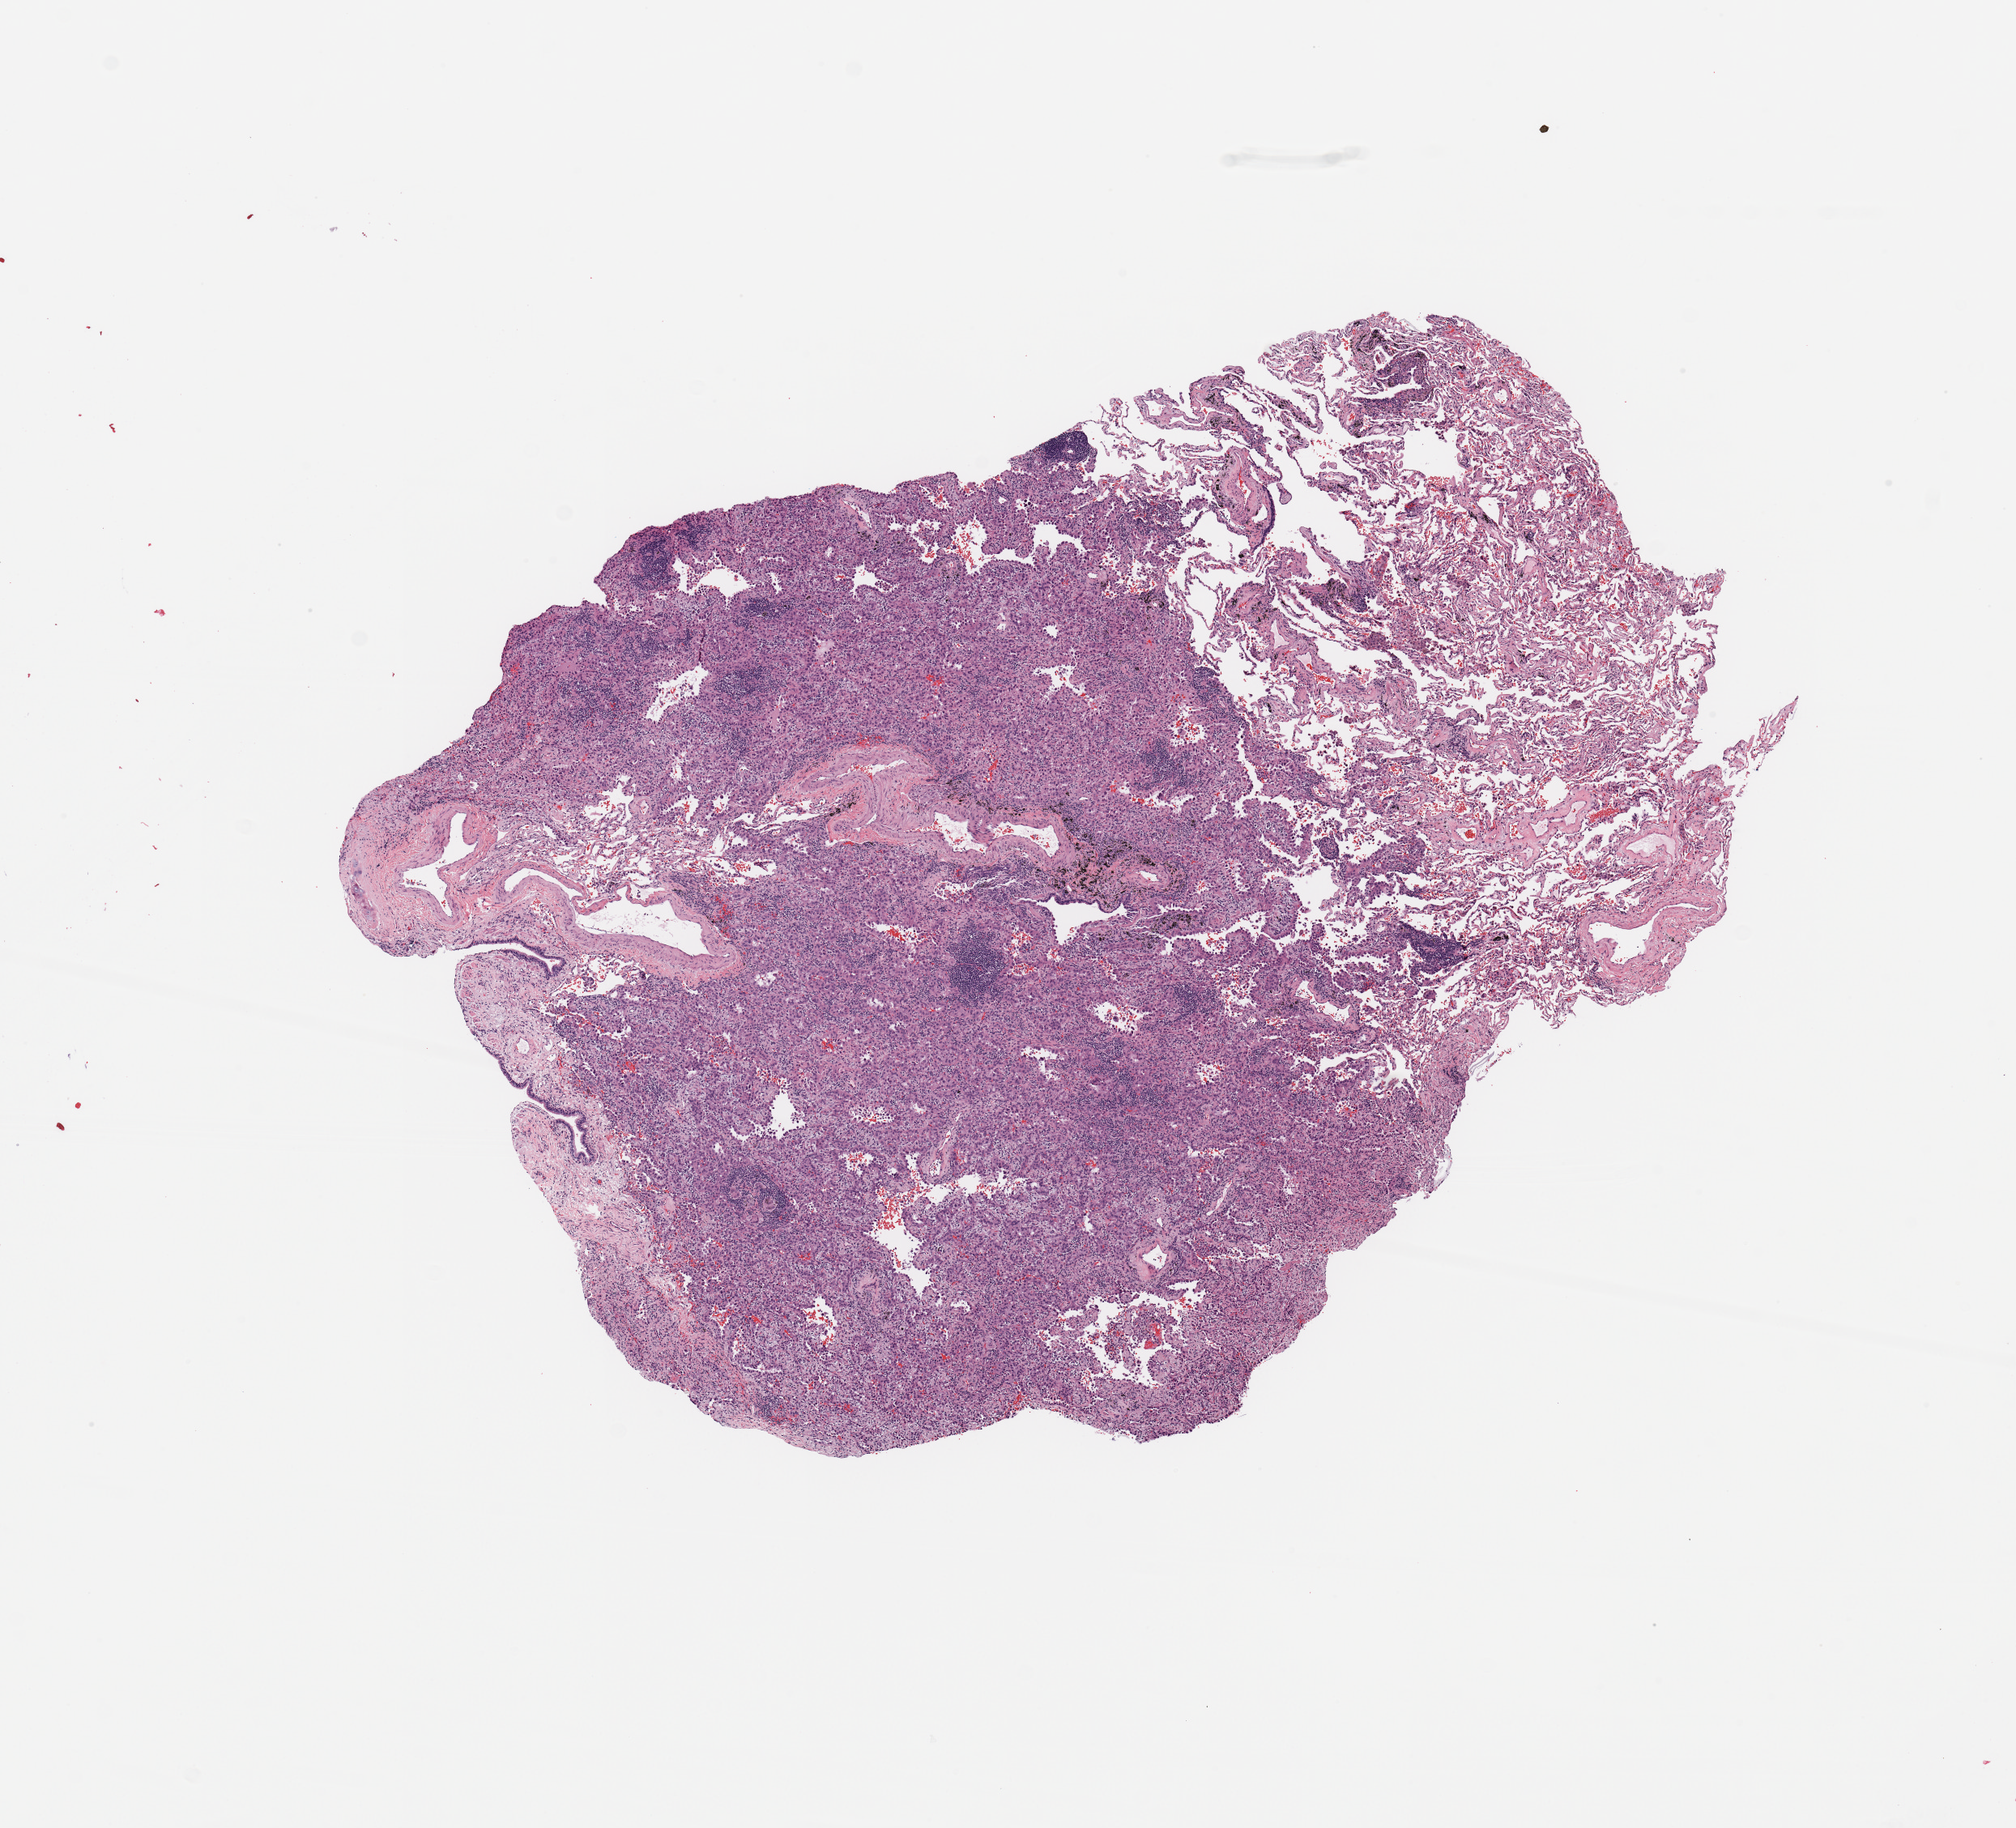
Whole-slide histology image, Hematoxylin and eosin (H&E) stained, shown as a low-resolution overview of the whole scanned area (about 9.8 x 8.9 mm); tumour tissue sample, sampled site: lung. Patient: female, age 78 years. Histologic grade: G2 (moderately differentiated). Pathologist review of this section (percent, as recorded): tumour nuclei 60%, necrosis 2%.
AJCC pathologic stage: IB. Primary tumour site (as recorded): left upper lobe. Histologic diagnosis: Adenocarcinoma, NOS.